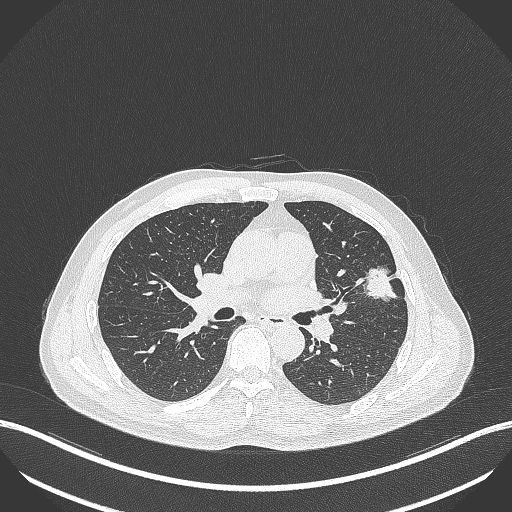
Chest CT, one axial slice. Position 220 of 418 along the scan axis. Reconstruction kernel B70f. Lung window (W 1500 / L -600 HU). 512 × 512 image matrix, field of view 400 × 400 mm. Male patient, age 55 years. Case-level facts recorded for this patient, not image findings: clinical TNM (as recorded): T1c N0 M0.
Structures marked on this image (bounding box drawn by a radiologist):
- lung tumour (recorded histology: adenocarcinoma): bounding box [x1, y1, x2, y2] px = [364, 263, 400, 303]